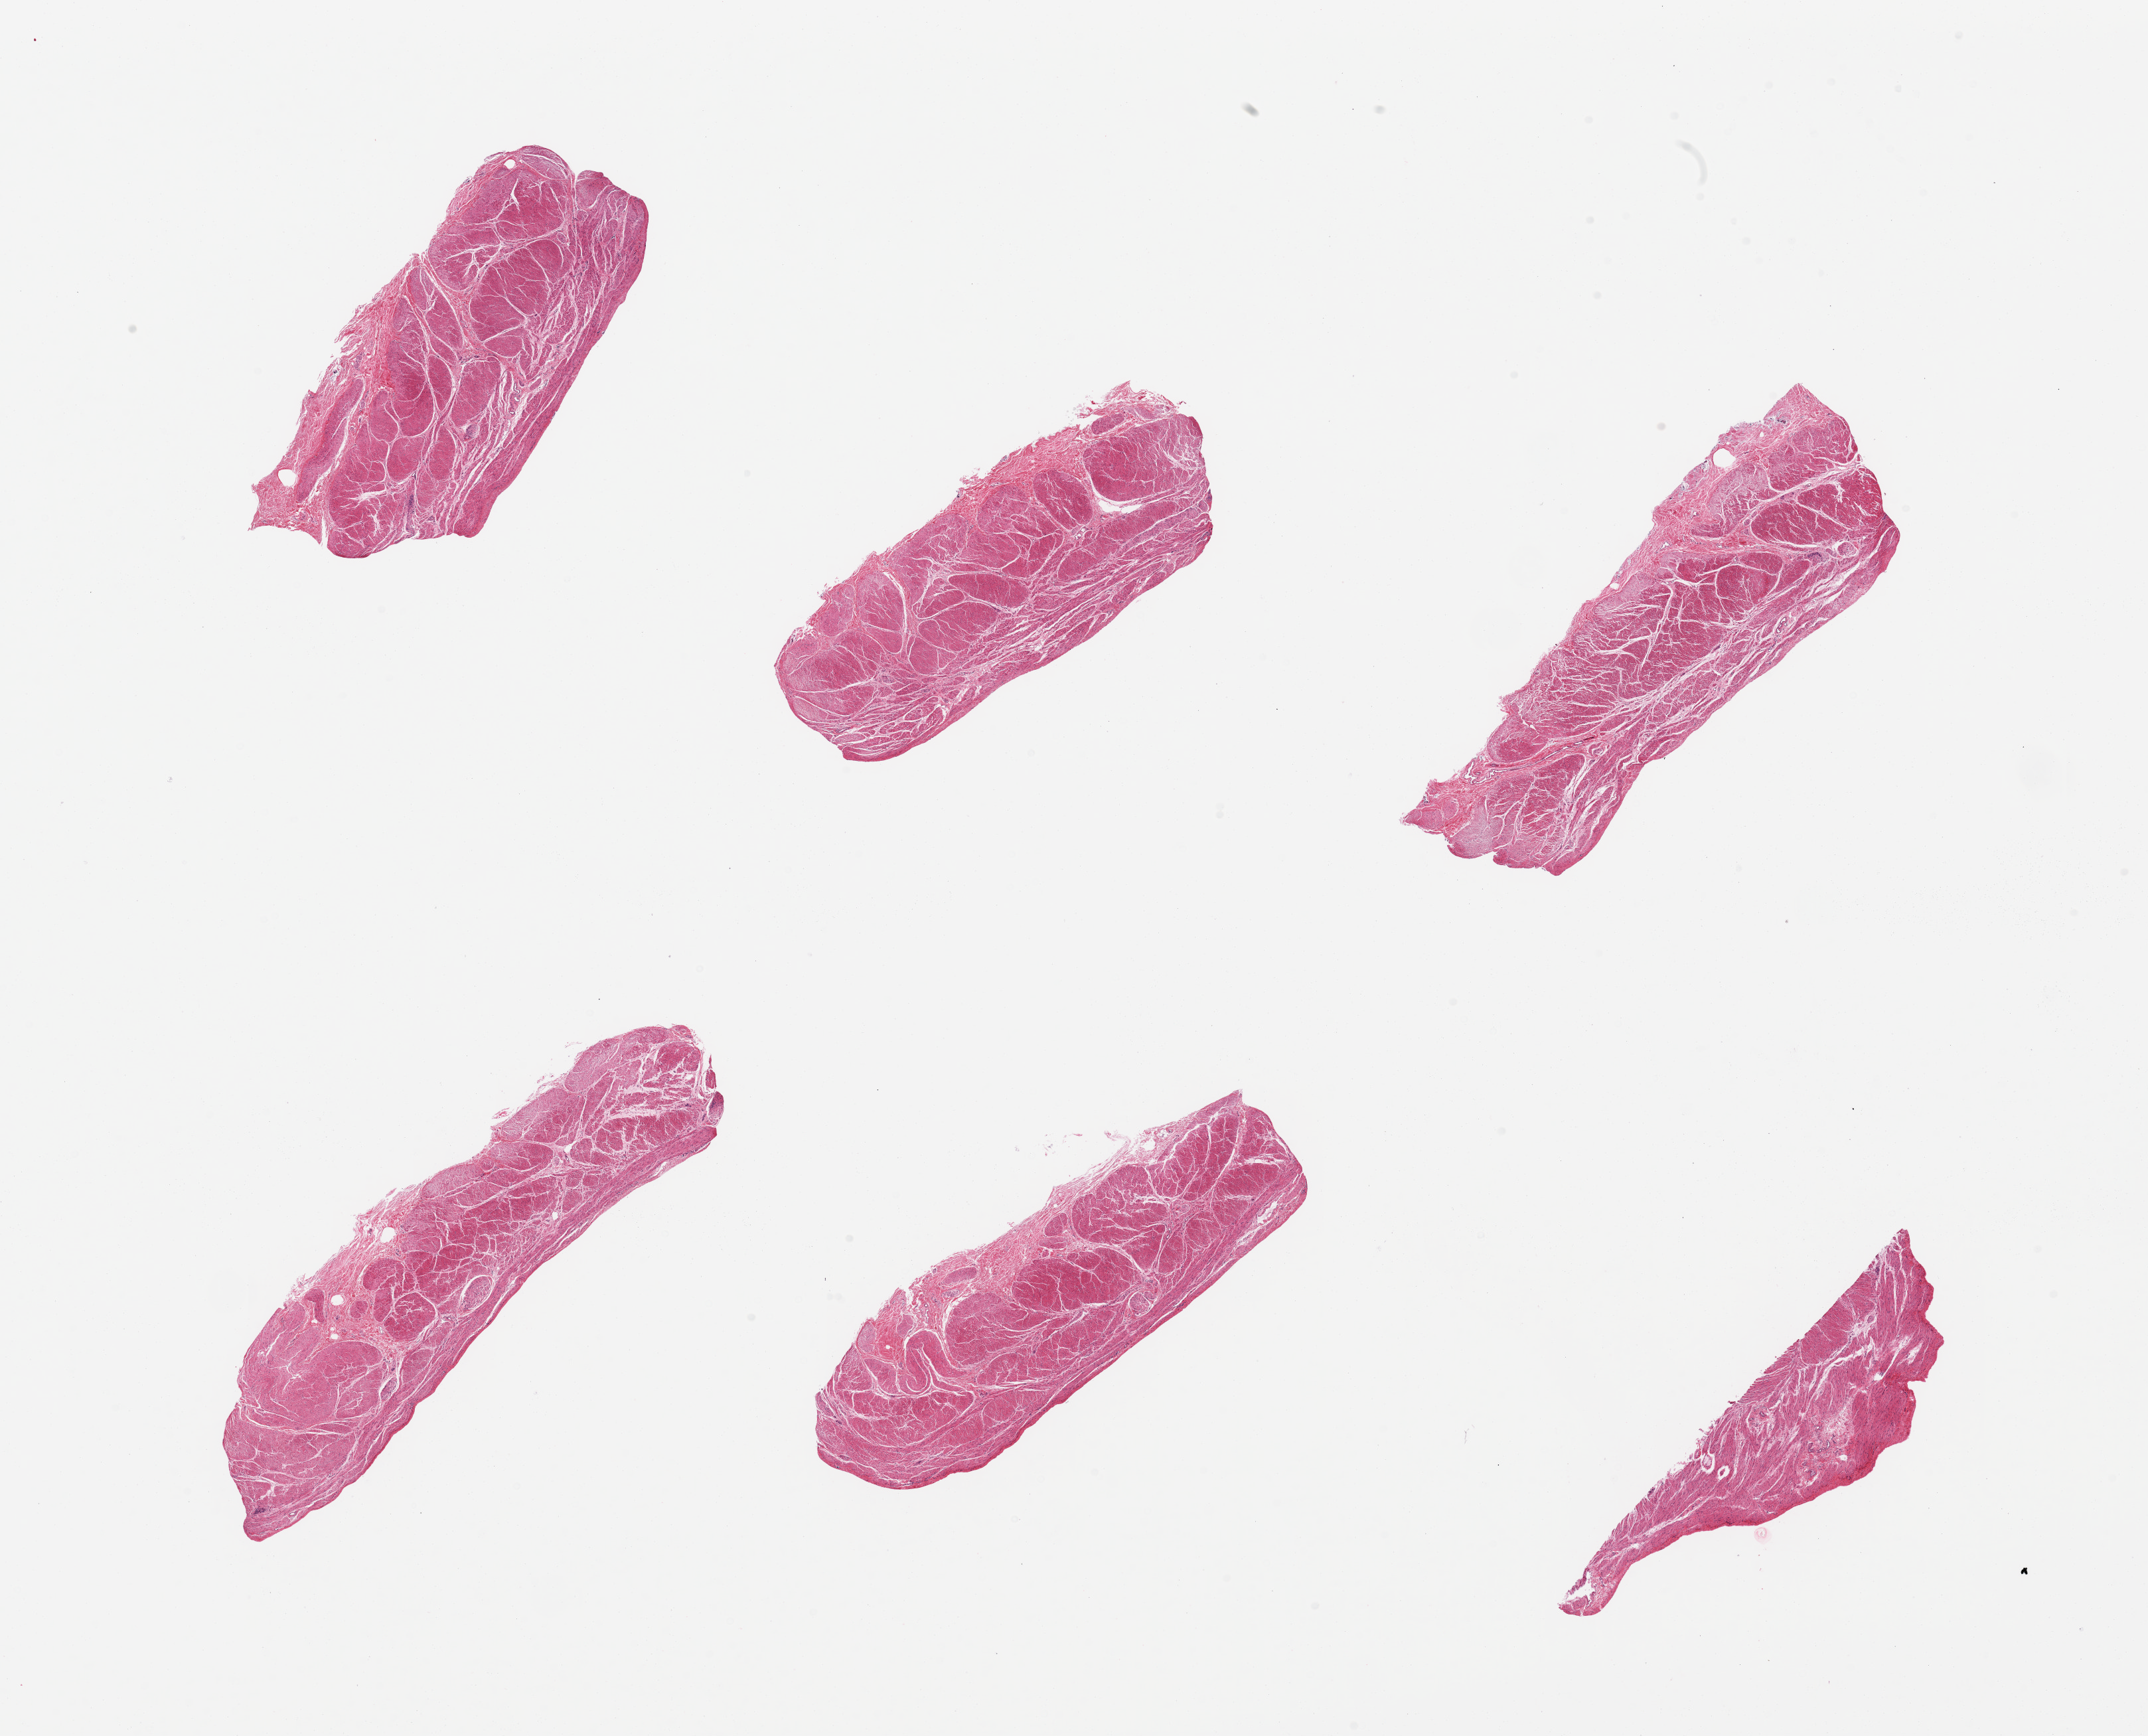
Whole-slide image, H&E stain — whole scanned area (about 25.6 x 20.7 mm) shown as a low-resolution overview. PAXgene-fixed paraffin-embedded (PFPE) section. Sampled site (target tissue): stomach. Donor tissue sample.
Reviewer comment on this tissue sample: 6 pieces; only muscularis; no target gastric mucosa included.